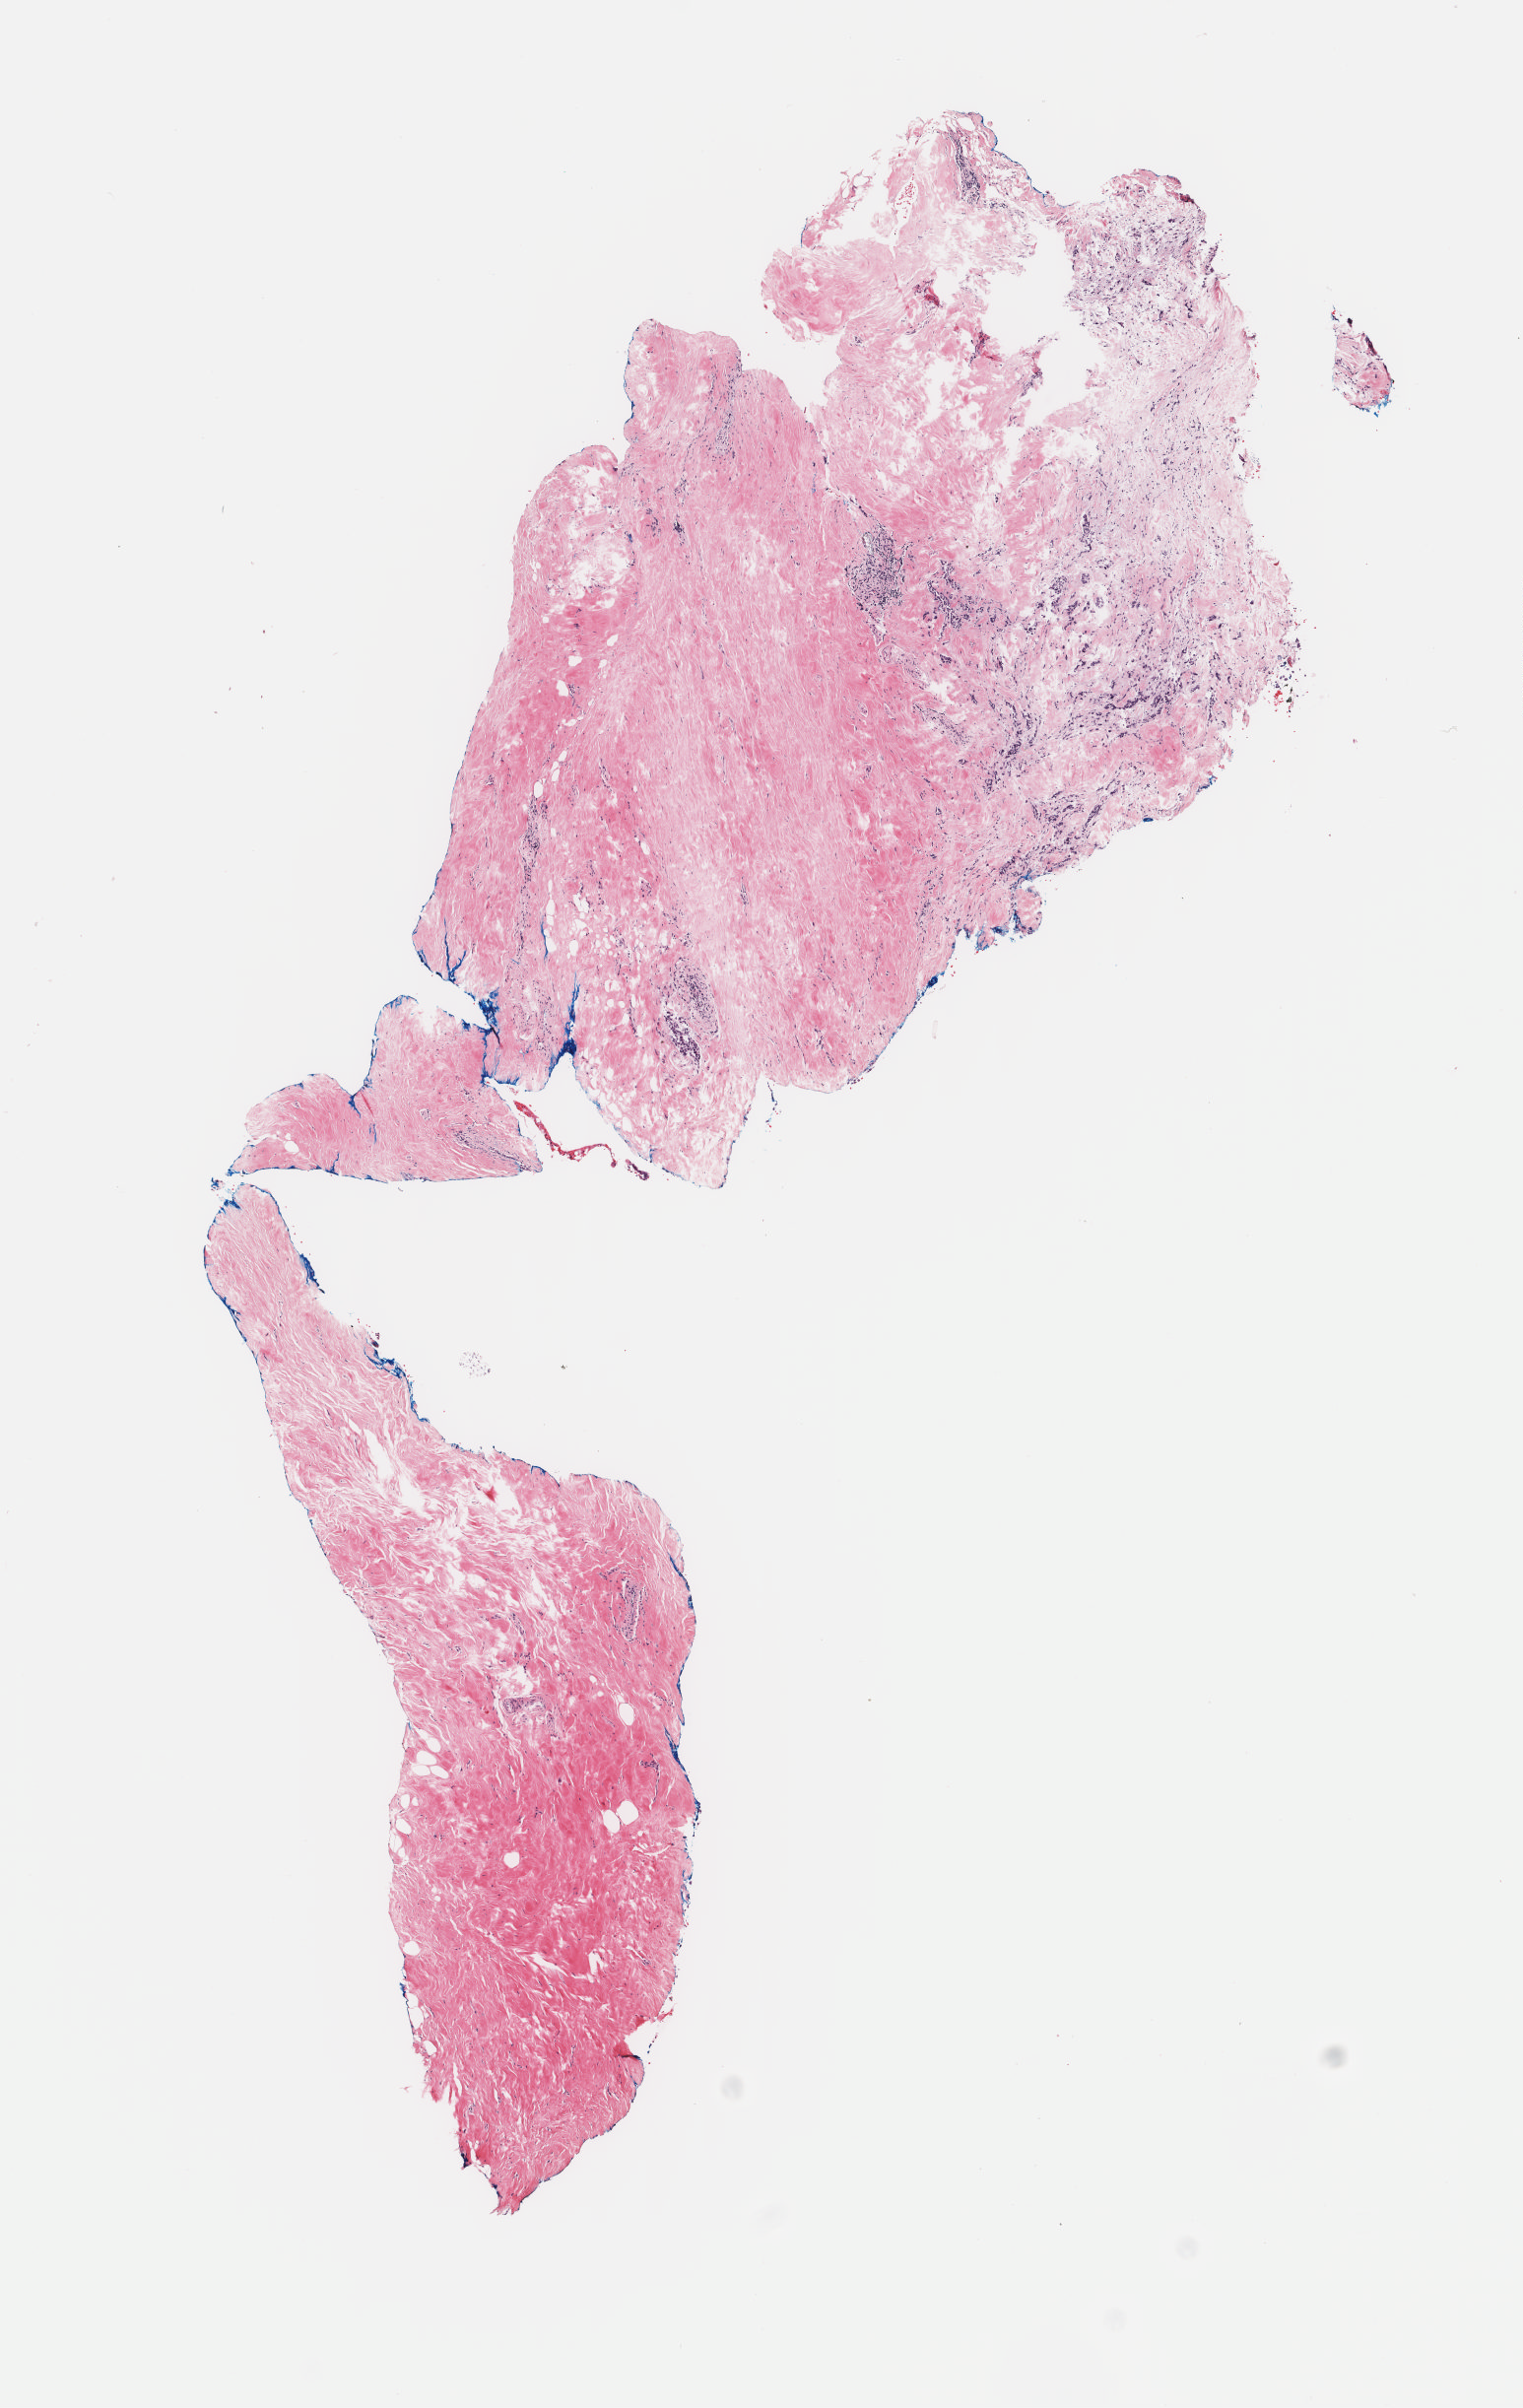
Digitized H&E tissue section (whole slide) — shown as a low-resolution overview of the whole scanned area (about 6.1 x 9.7 mm, slide scanned at 40x); frozen section; breast, primary tumour sample. Patient: female, age at initial diagnosis 53 years. Slide review estimates, as recorded: tumour cells 20%, tumour nuclei 30%, normal cells 1%, stromal cells 79%, necrosis 0%. Infiltration values recorded for this section: lymphocyte infiltration 0%, monocyte infiltration 0%, neutrophil infiltration 0%.
- pathologic diagnosis: Lobular carcinoma, NOS
- AJCC pathologic stage: IA
- TNM: T1c N0 (i-) MX
- lymph nodes positive (case pathology): 0 of 5 examined